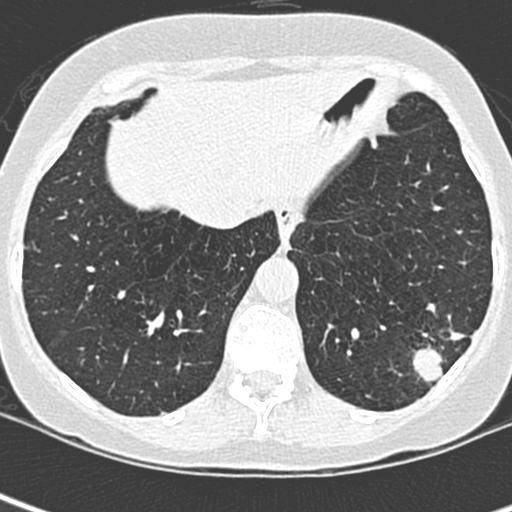
Low-dose screening chest CT, one axial slice; slice 70 of 252 in the series (ordered by position); lung window (W 1500 / L -600 HU); 1.3 mm slice thickness; 512 × 512 image matrix, field of view 271 × 271 mm.
Outlined on this slice (manually delineated by an expert):
- lesion 1 (tumor, lower lobe of left lung): bounding box (x1, y1, x2, y2) in pixels: (412, 328, 465, 385)